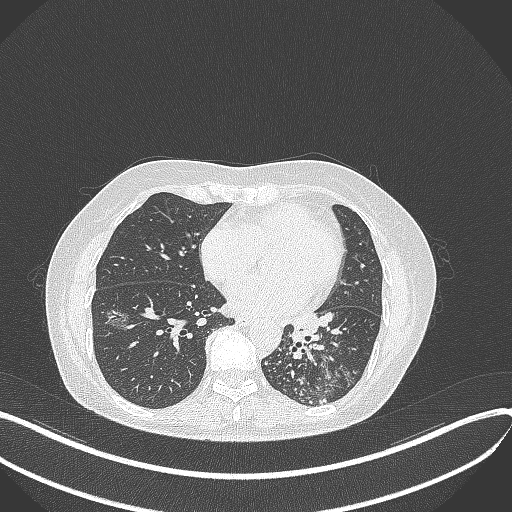
Chest CT, one axial slice. Reconstruction kernel B70f. 100 kVp. Lung window (W 1500 / L -600 HU). 1 mm slice thickness. 512 × 512 image matrix, field of view 400 × 400 mm. Female patient, age 63 years. Case-level facts recorded for this patient, not image findings: clinical TNM (as recorded): T1b N0 M0; histopathological grade: G2-3.
Outlined on this slice (rectangle marked by the reading radiologist):
- lung tumour (recorded histology: adenocarcinoma): bounding box <289,310,325,343> (left, top, right, bottom; pixels)